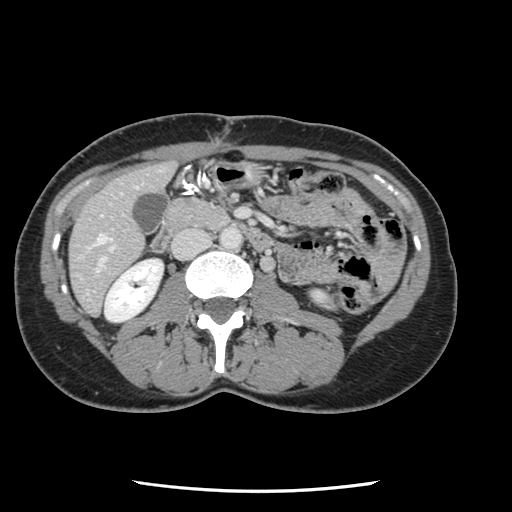
Contrast-enhanced abdominal CT, one axial slice. Slice 30 of 134 in the series (ordered by position). 120 kVp. Intravenous contrast given. Soft-tissue window (W 400 / L 40 HU). 512 × 512 image matrix, field of view 330 × 330 mm. Female patient, age 43 years. From the clinical record (not read from this slice): diagnosis: colorectal cancer liver metastases, imaged before liver resection; multiple liver metastases: yes; largest metastasis: 3.4 cm; disease in both lobes: yes.
Structures marked on this image (expert manual segmentation):
- hepatic veins: bounding box <96,234,111,244> (left, top, right, bottom; pixels)
- liver: <70,163,175,315>
- planned liver remnant (the part of the liver to remain after resection): <70,163,174,314>